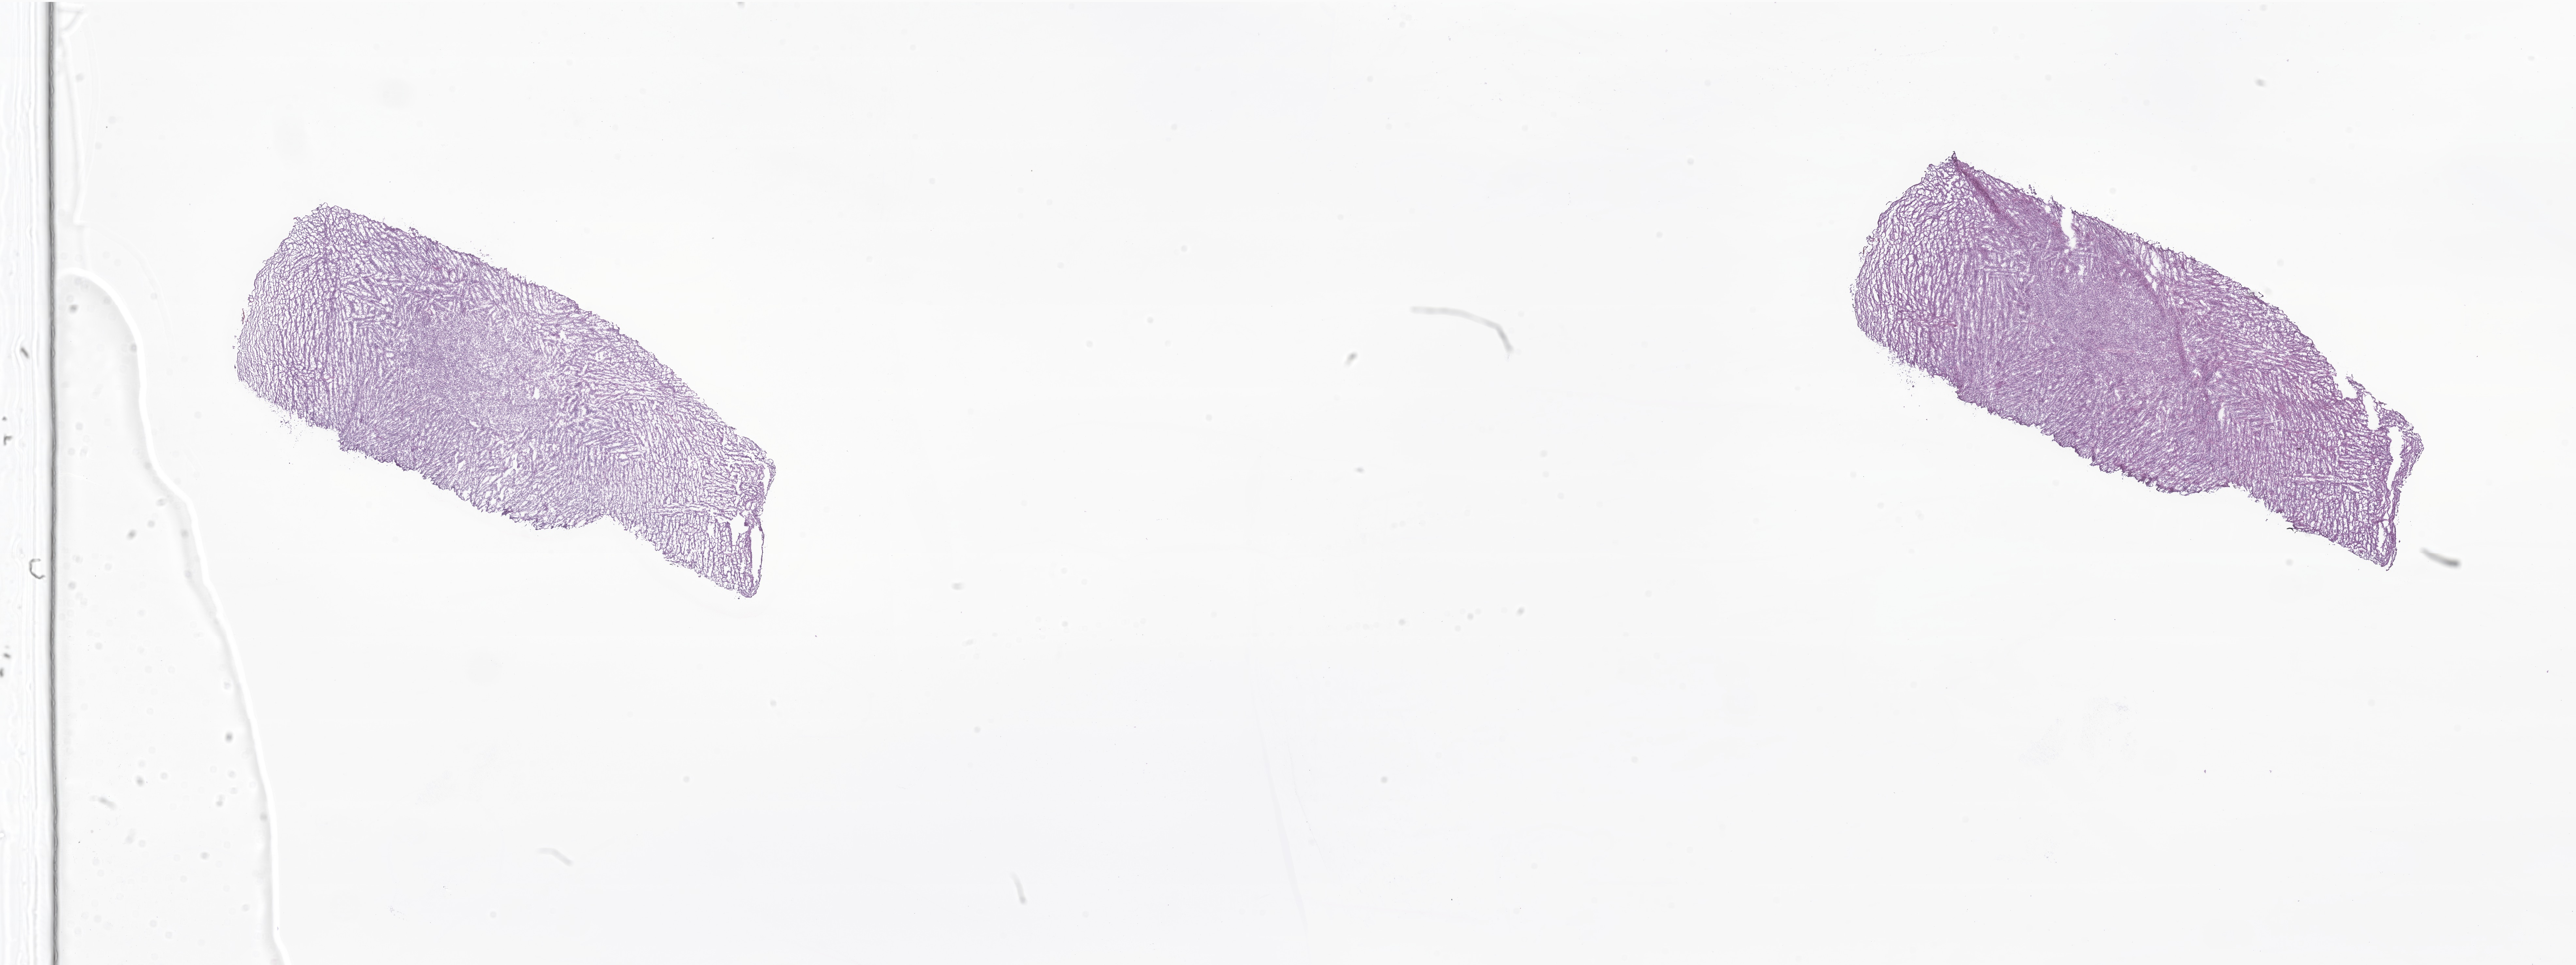
Digitized H&E-stained section of tumor tissue from the brain, a low-resolution overview of the entire scanned area, about 33.3 x 12.5 mm. Cryosection (OCT / tissue freezing medium). Patient: female, age 74 months.
Diagnosis: Medulloblastoma, NOS.